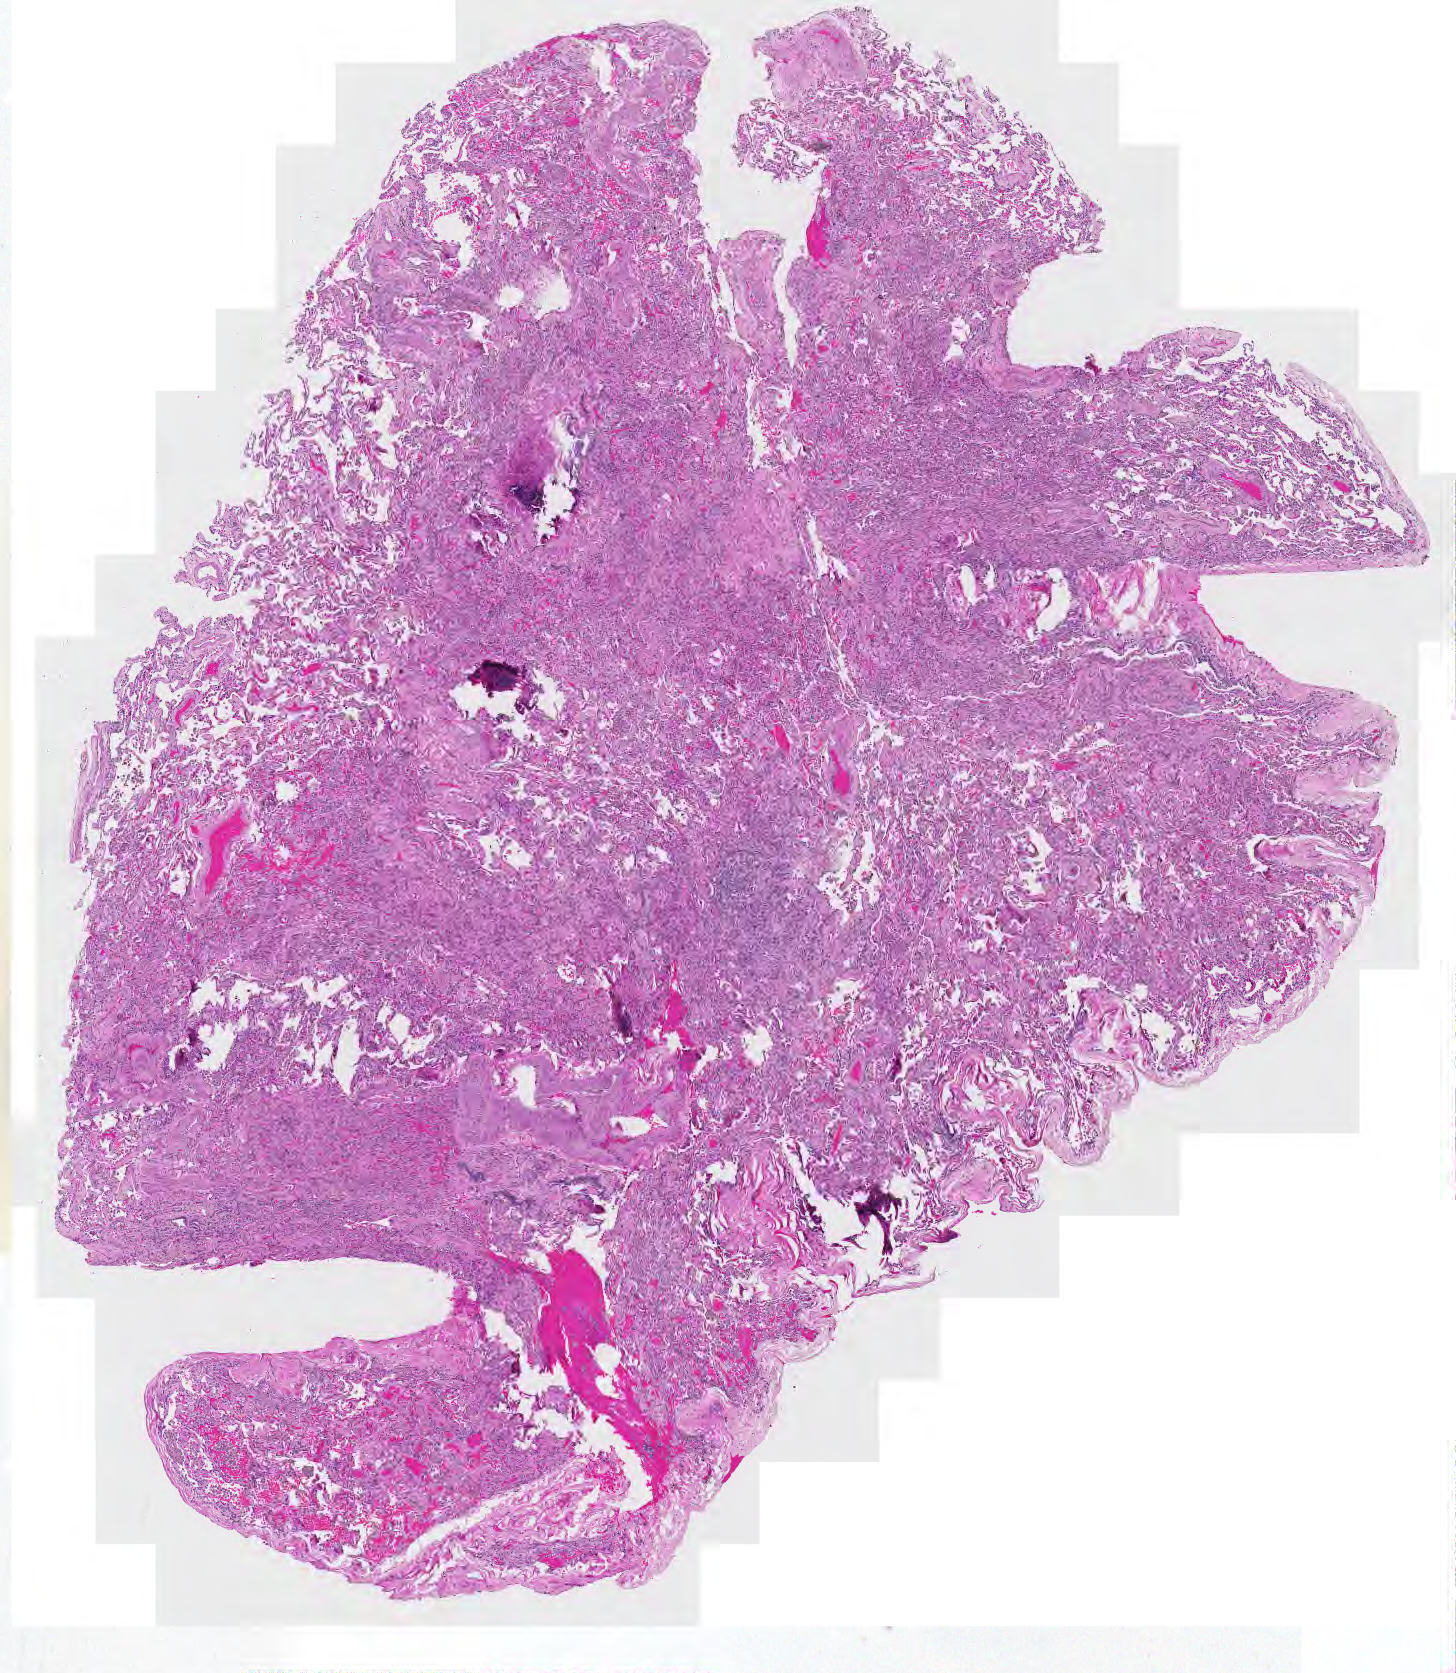
Digitized H&E tissue section (whole slide) — shown as a low-resolution overview of the whole scanned area (about 7.5 x 8.6 mm, slide scanned at 20x). Normal (non-tumour) tissue sample, sampled site: lung. 68-year-old female patient.
• this section: normal (non-tumour) tissue from the same patient
• patient diagnosis: Adenocarcinoma, NOS